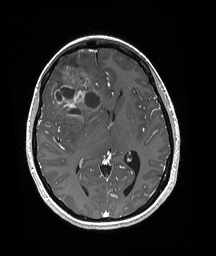
Brain MRI from a brain-tumour surgery series, one axial slice. Slice 98 of 192 in the series (ordered by position). T1-weighted post-contrast. 1 mm slice thickness. 216 × 256 image matrix, field of view 211 × 250 mm. Case-level facts recorded for this patient, not image findings: histopathology: Oligodendroglioma; WHO grade: 3; IDH mutation: yes; tumour location: Right Frontal.
Outlined on this slice (outlined manually by an expert reader):
- tumour: box from (x=47, y=56) to (x=101, y=118) px